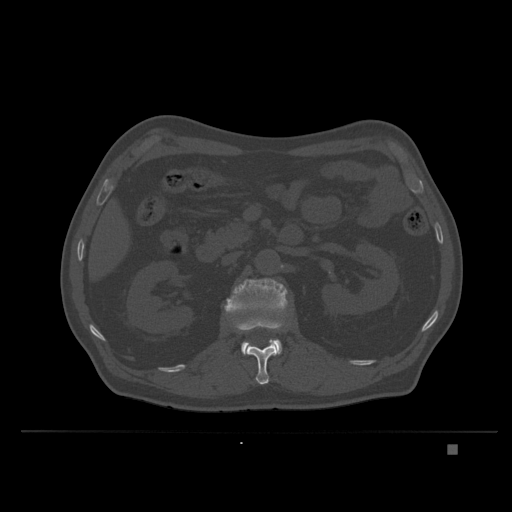
CT including the spine, one axial slice. Slice 129 of 435 in the series (ordered by position). Bone window (W 1800 / L 400 HU). 512 × 512 image matrix, field of view 434 × 434 mm. Patient: male, 73 years. Case-level facts recorded for this patient, not image findings: primary cancer: skin.
Annotated regions visible in this slice (semi-automatic segmentation, software-assisted and operator-edited):
- L1 vertebra: bounding box [x1, y1, x2, y2] px = [241, 328, 278, 385]
- L2 vertebra: [225, 278, 291, 355]